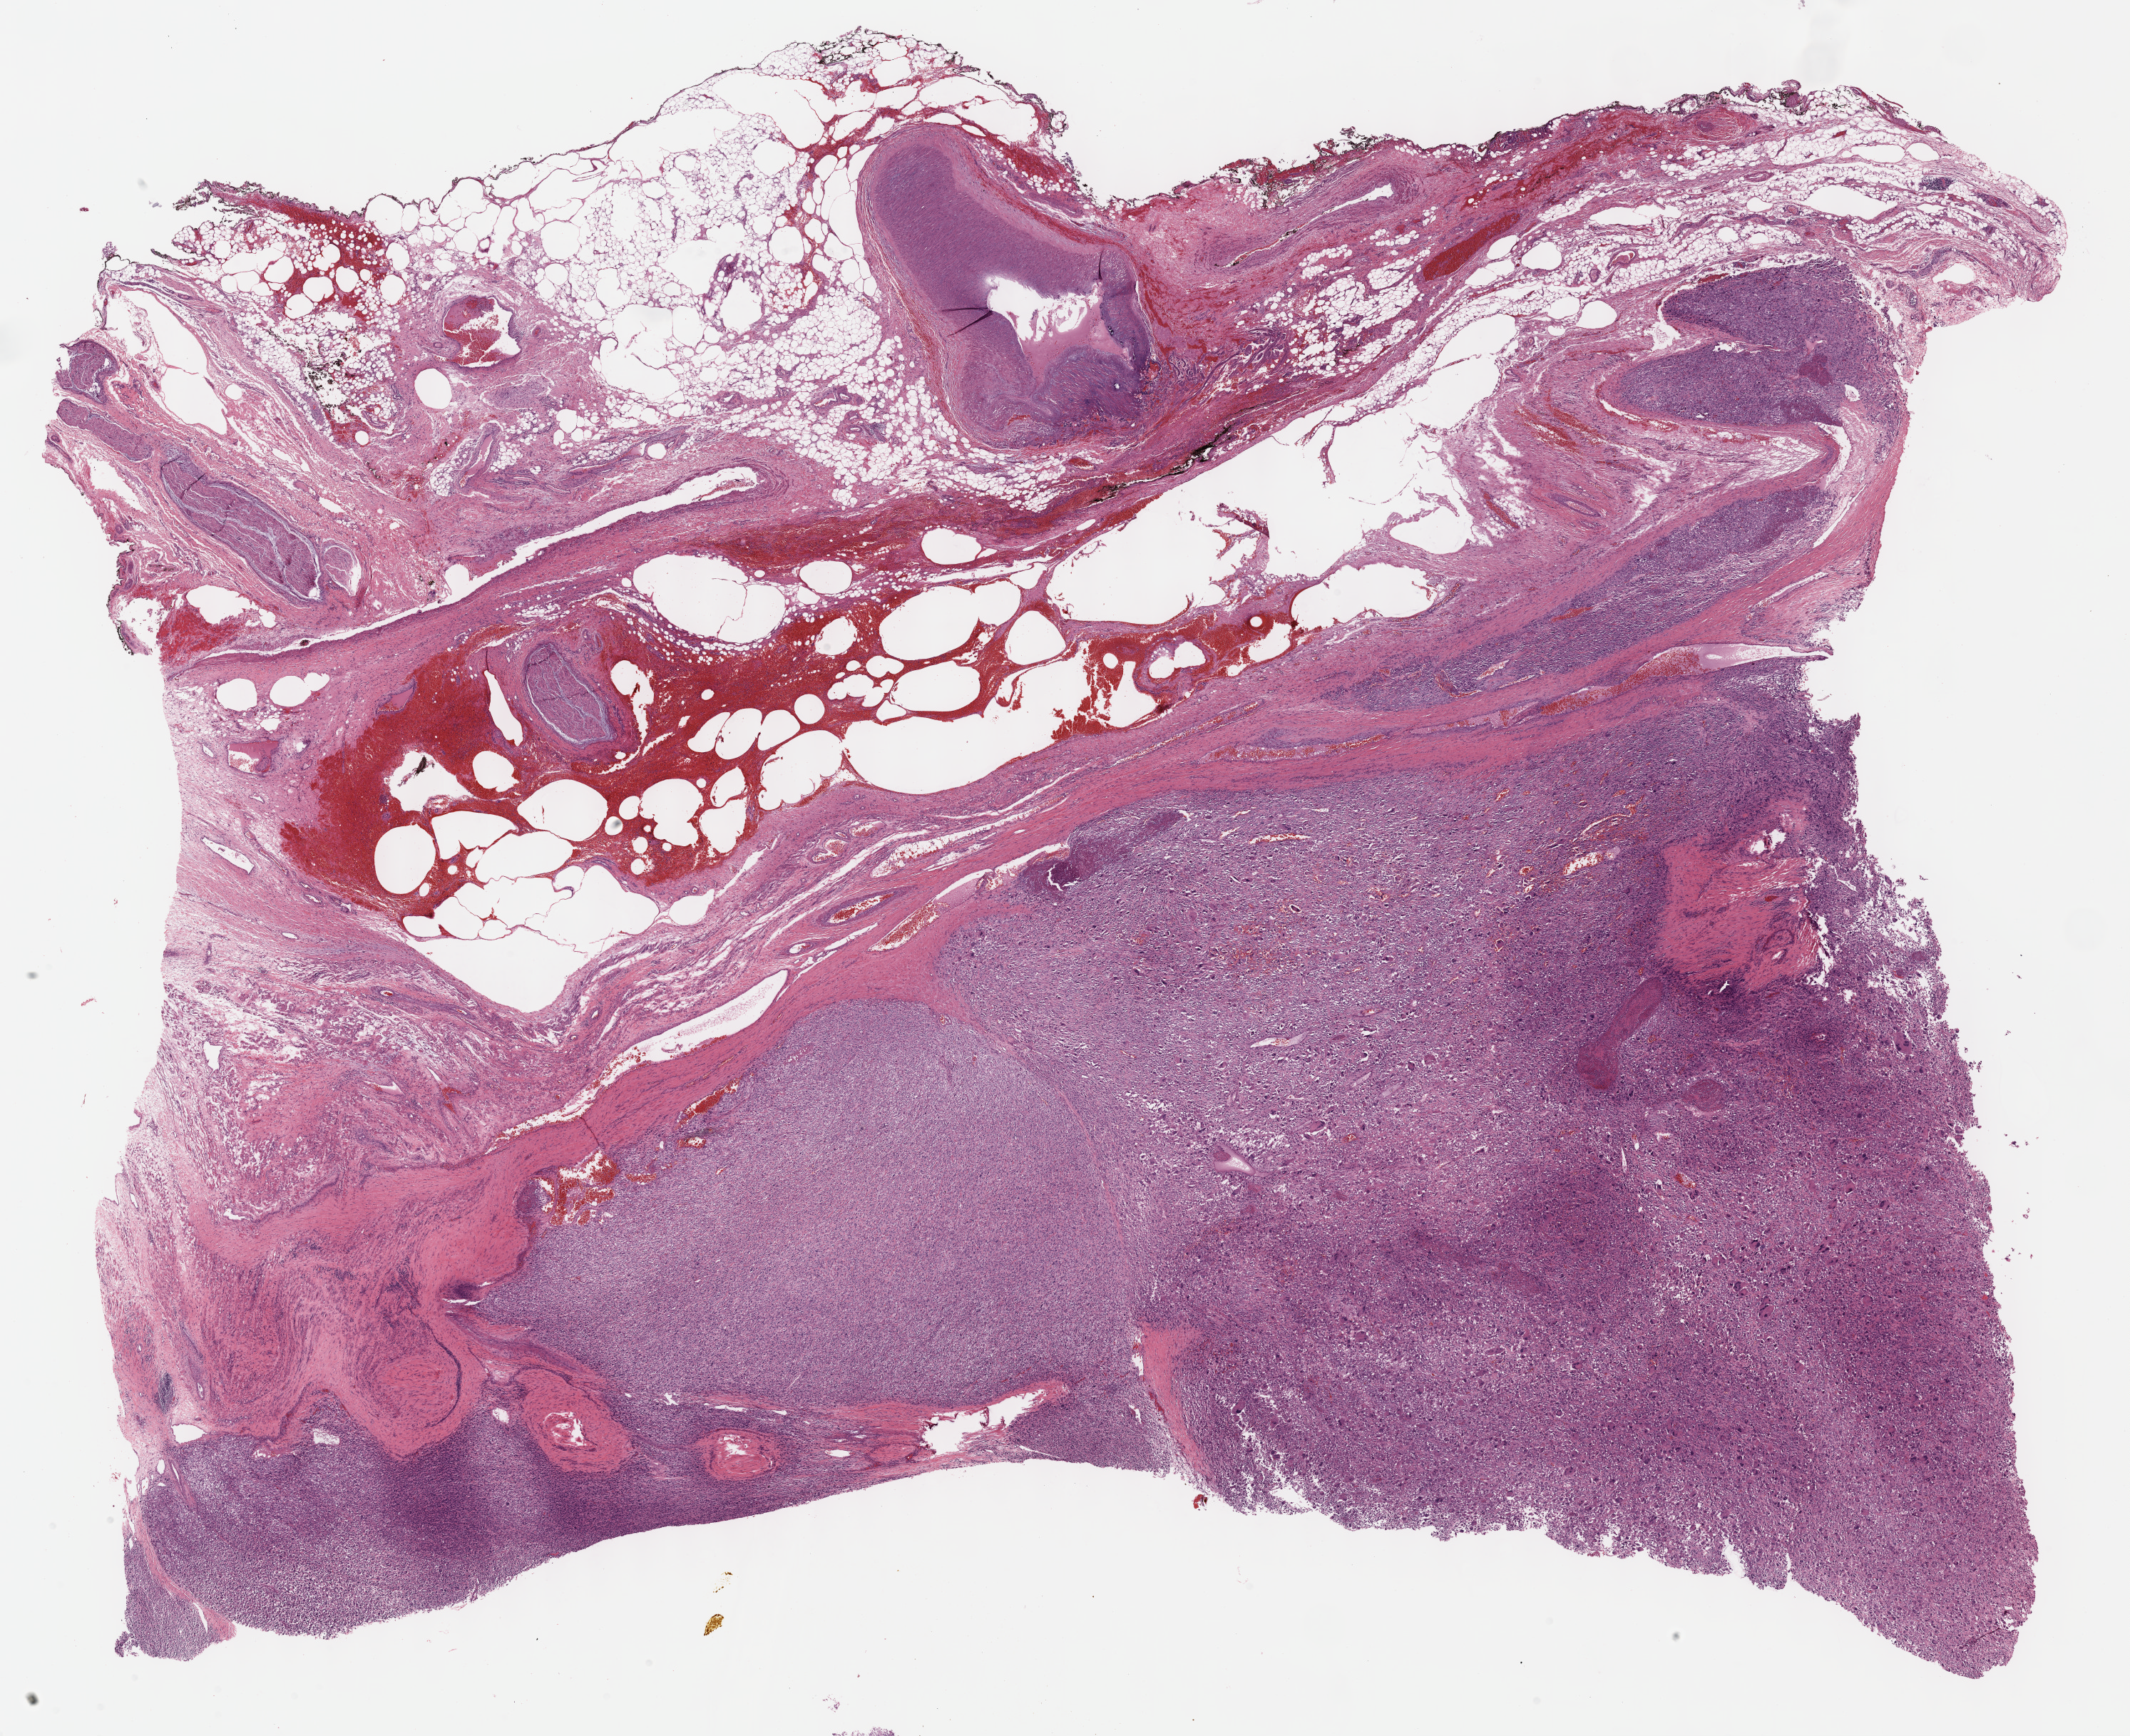
H&E-stained whole-slide image, a low-resolution overview of the entire scanned area, about 24.2 x 19.7 mm, FFPE section, sample: primary tumour, connective, subcutaneous and other soft tissues. Patient: female, age at initial diagnosis 68 years.
Histologic diagnosis: Undifferentiated sarcoma (connective, subcutaneous and other soft tissues of lower limb and hip).